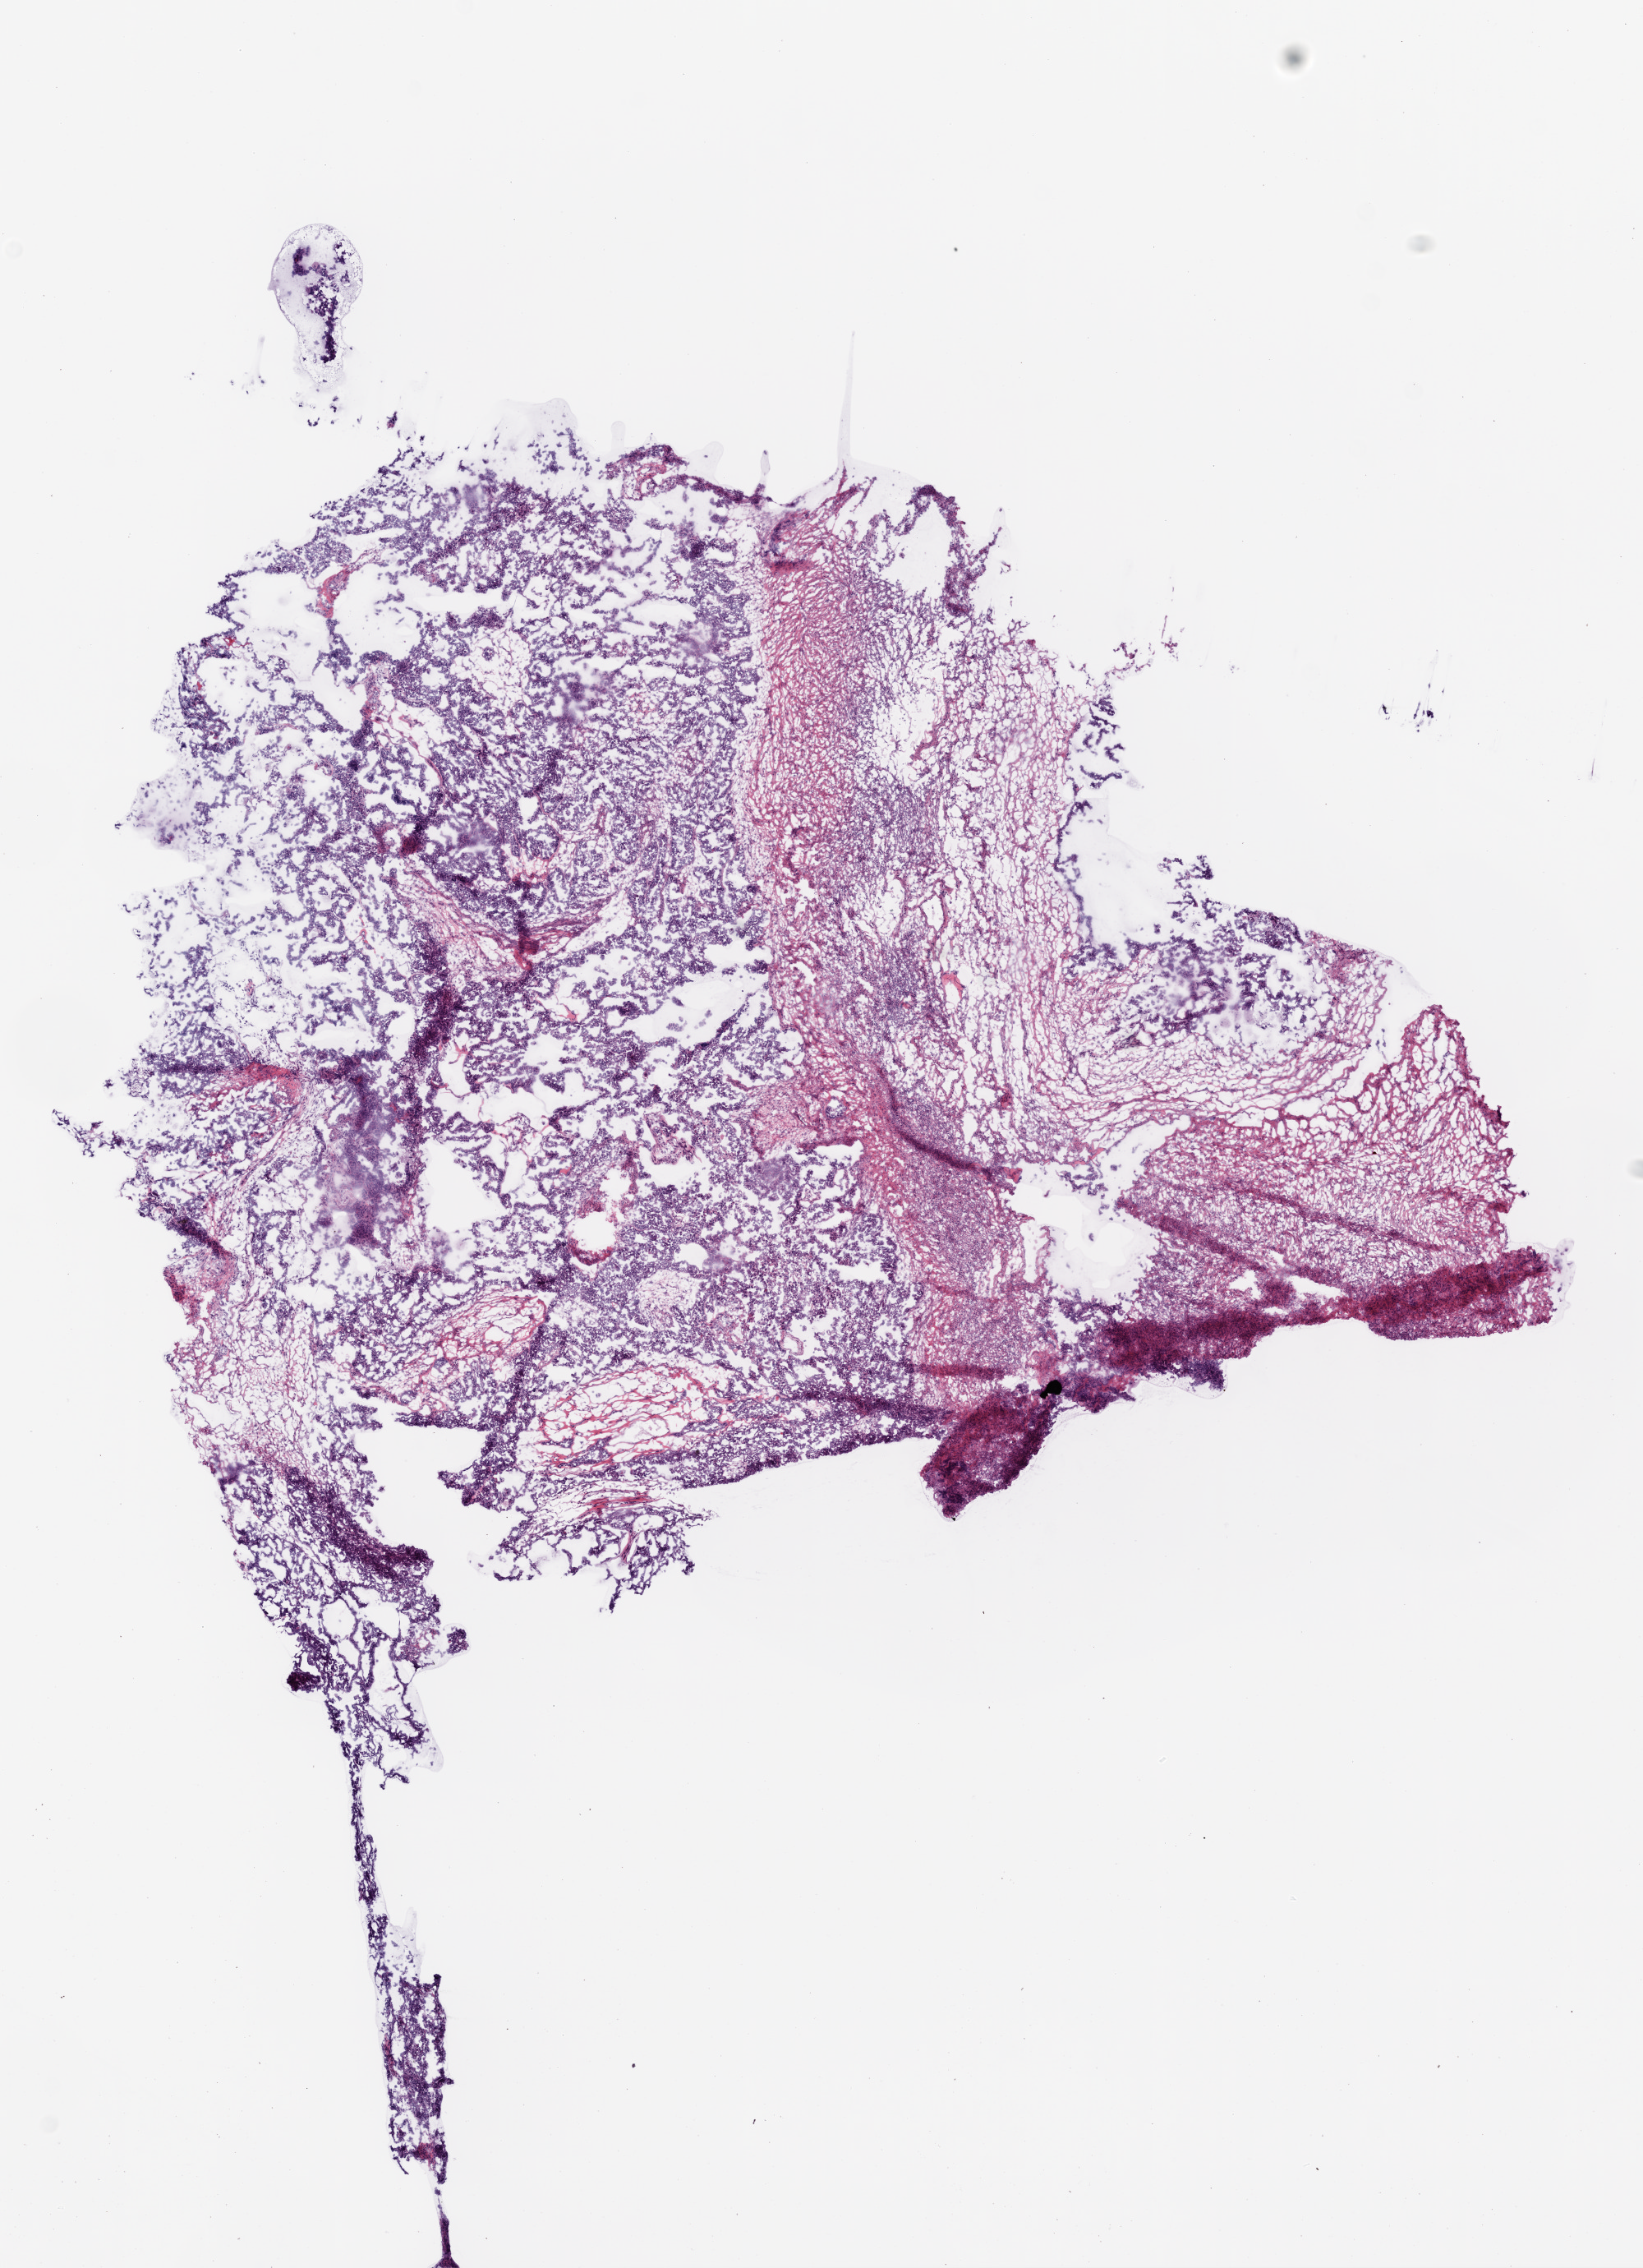
Whole-slide histology image, Hematoxylin and eosin (H&E) stained, a low-resolution overview of the entire scanned area, about 8.0 x 11.1 mm (from a 20x scan), frozen section from the top of the tissue portion, sample: primary tumour, ovary. Patient: female, age at initial diagnosis 55 years. Histologic grade: G3 (poorly differentiated). Pathologist review of this section (percent, as recorded): tumour cells 80%, tumour nuclei 80%, normal cells 0%, stromal cells 20%, necrosis 0%.
- pathologic diagnosis: Serous cystadenocarcinoma, NOS
- FIGO stage: IIIC